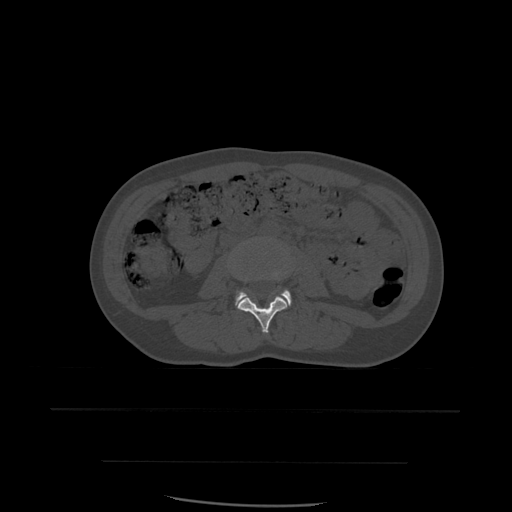
CT including the spine, one axial slice; position 187 of 574 along the scan axis; bone window (W 1800 / L 400 HU); 1.25 mm slice thickness; 512 × 512 image matrix, field of view 392 × 392 mm. Patient age 48 years. From the clinical record (not read from this slice): primary cancer: lung.
Structures marked on this image (semi-automatic segmentation, software-assisted and operator-edited):
- L3 vertebra: bounding box <238,297,288,334> (left, top, right, bottom; pixels)
- L4 vertebra: <236,290,292,306>